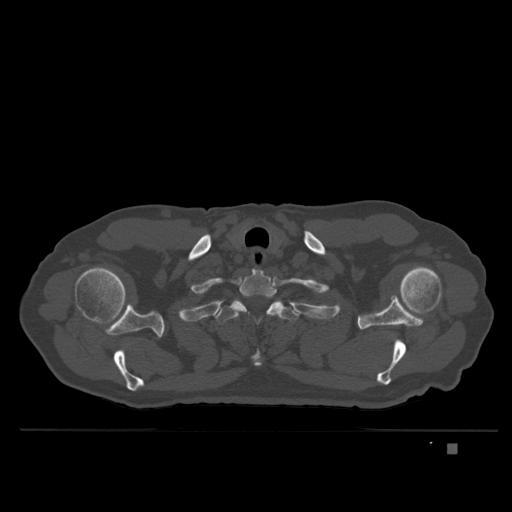
CT including the spine, one axial slice. Slice 318 of 435 in the series (ordered by position). Bone window (W 1800 / L 400 HU). 1.5 mm slice thickness. 512 × 512 image matrix, field of view 434 × 434 mm. Male patient, age 73 years. From the clinical record (not read from this slice): primary cancer: skin.
Outlined on this slice (semi-automatically segmented with operator editing):
- T1 vertebra: bounding box (x1, y1, x2, y2) in pixels: (237, 269, 284, 317)
- T2 vertebra: (216, 293, 297, 366)